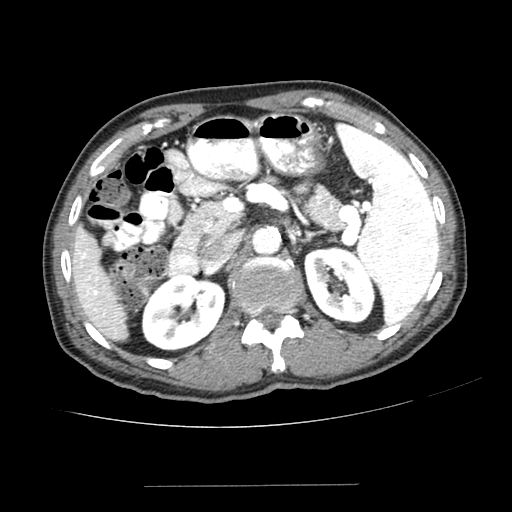
Contrast-enhanced abdominal CT (liver protocol), one axial slice; position 140 of 187 along the scan axis; reconstruction kernel SOFT; 100 kVp; one of 2 acquisitions stored at this slice position; soft-tissue window (W 400 / L 40 HU); 2.5 mm slice thickness; 512 × 512 image matrix, field of view 360 × 360 mm. From the clinical record (not read from this slice): diagnosis: hepatocellular carcinoma (patient treated with transarterial chemoembolisation; whether this scan precedes or follows treatment is not stated here); TNM stage (as recorded): Stage-I; Child-Pugh class: A; tumour differentiation: poorly differentiated; tumour nodularity: uninodular.
Outlined on this slice (semi-automatic segmentation, software-assisted and operator-edited):
- liver parenchyma outside the tumour (the mass and vessels are separate outlines, so this box may not span the whole liver): bounding box [x1, y1, x2, y2] px = [70, 224, 128, 340]
- liver vessels: [81, 252, 98, 311]